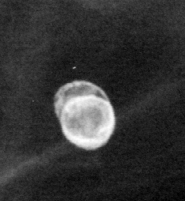
Cropped region of a digitized screen-film mammogram centred on a radiologist-marked abnormality, left breast, CC view.
- Calcifications, morphology lucent center; BI-RADS assessment category 2; benign without callback (not worked up further).